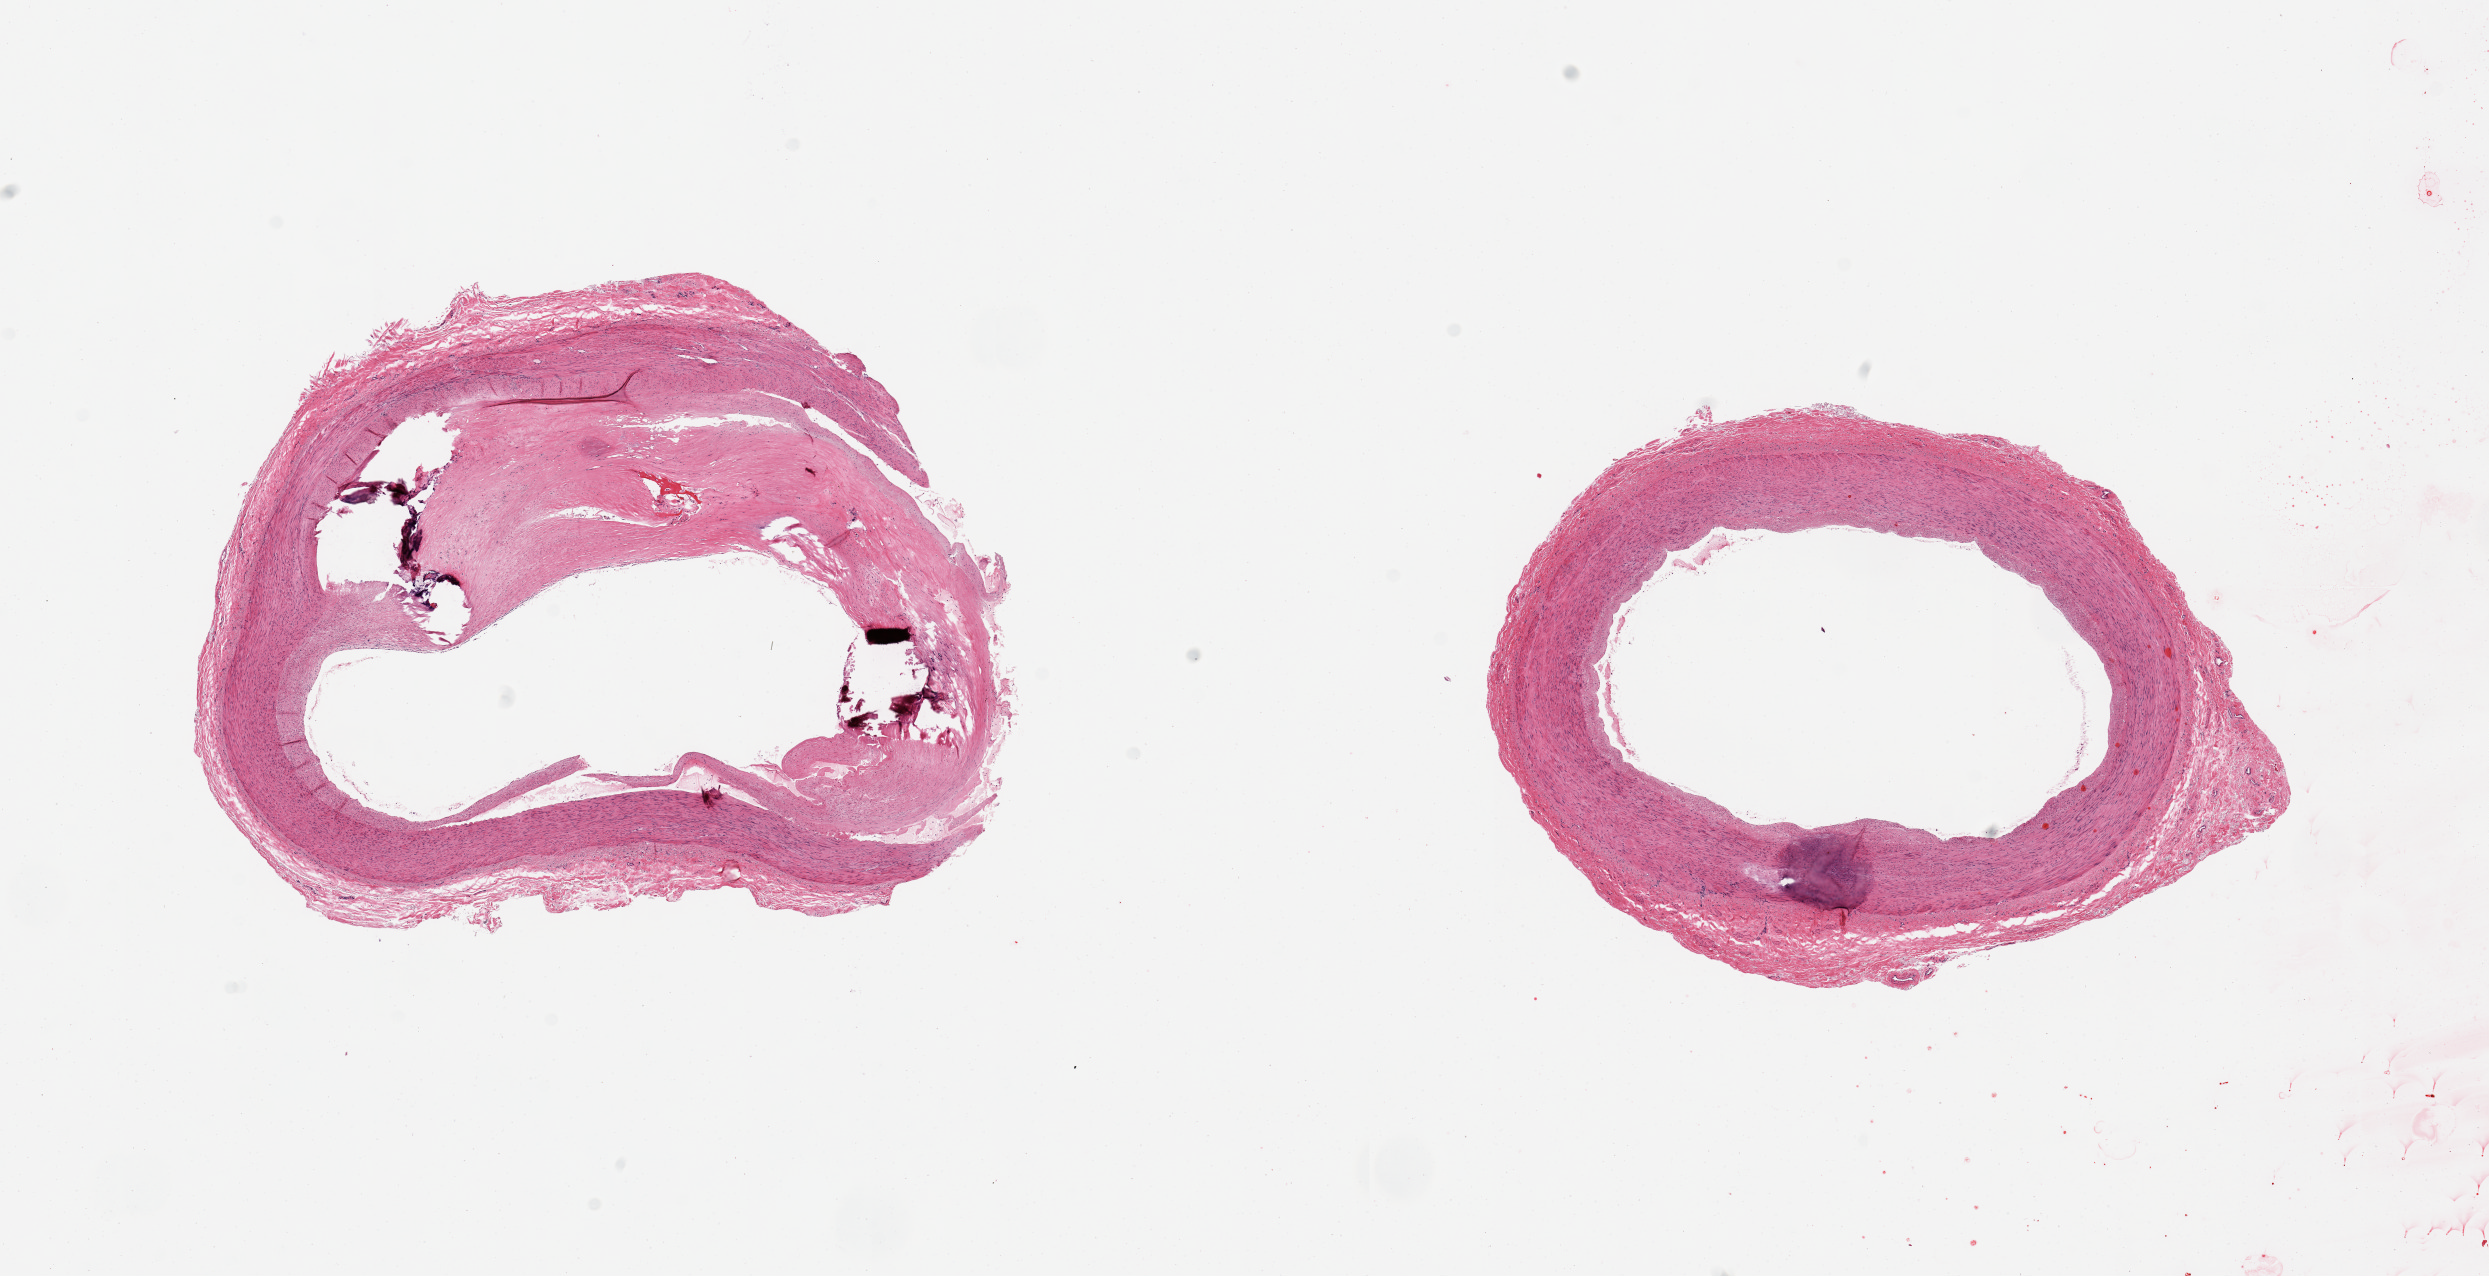
Haematoxylin and eosin whole-slide image — low-resolution overview of the scanned area, about 19.7 x 10.1 mm, PAXgene-fixed paraffin-embedded (PFPE) section, target tissue: tibial artery, tissue donor sample. Donor sex: male.
Review note (as recorded): 2 pieces, ~60% occlusive focally calcified atherosis.